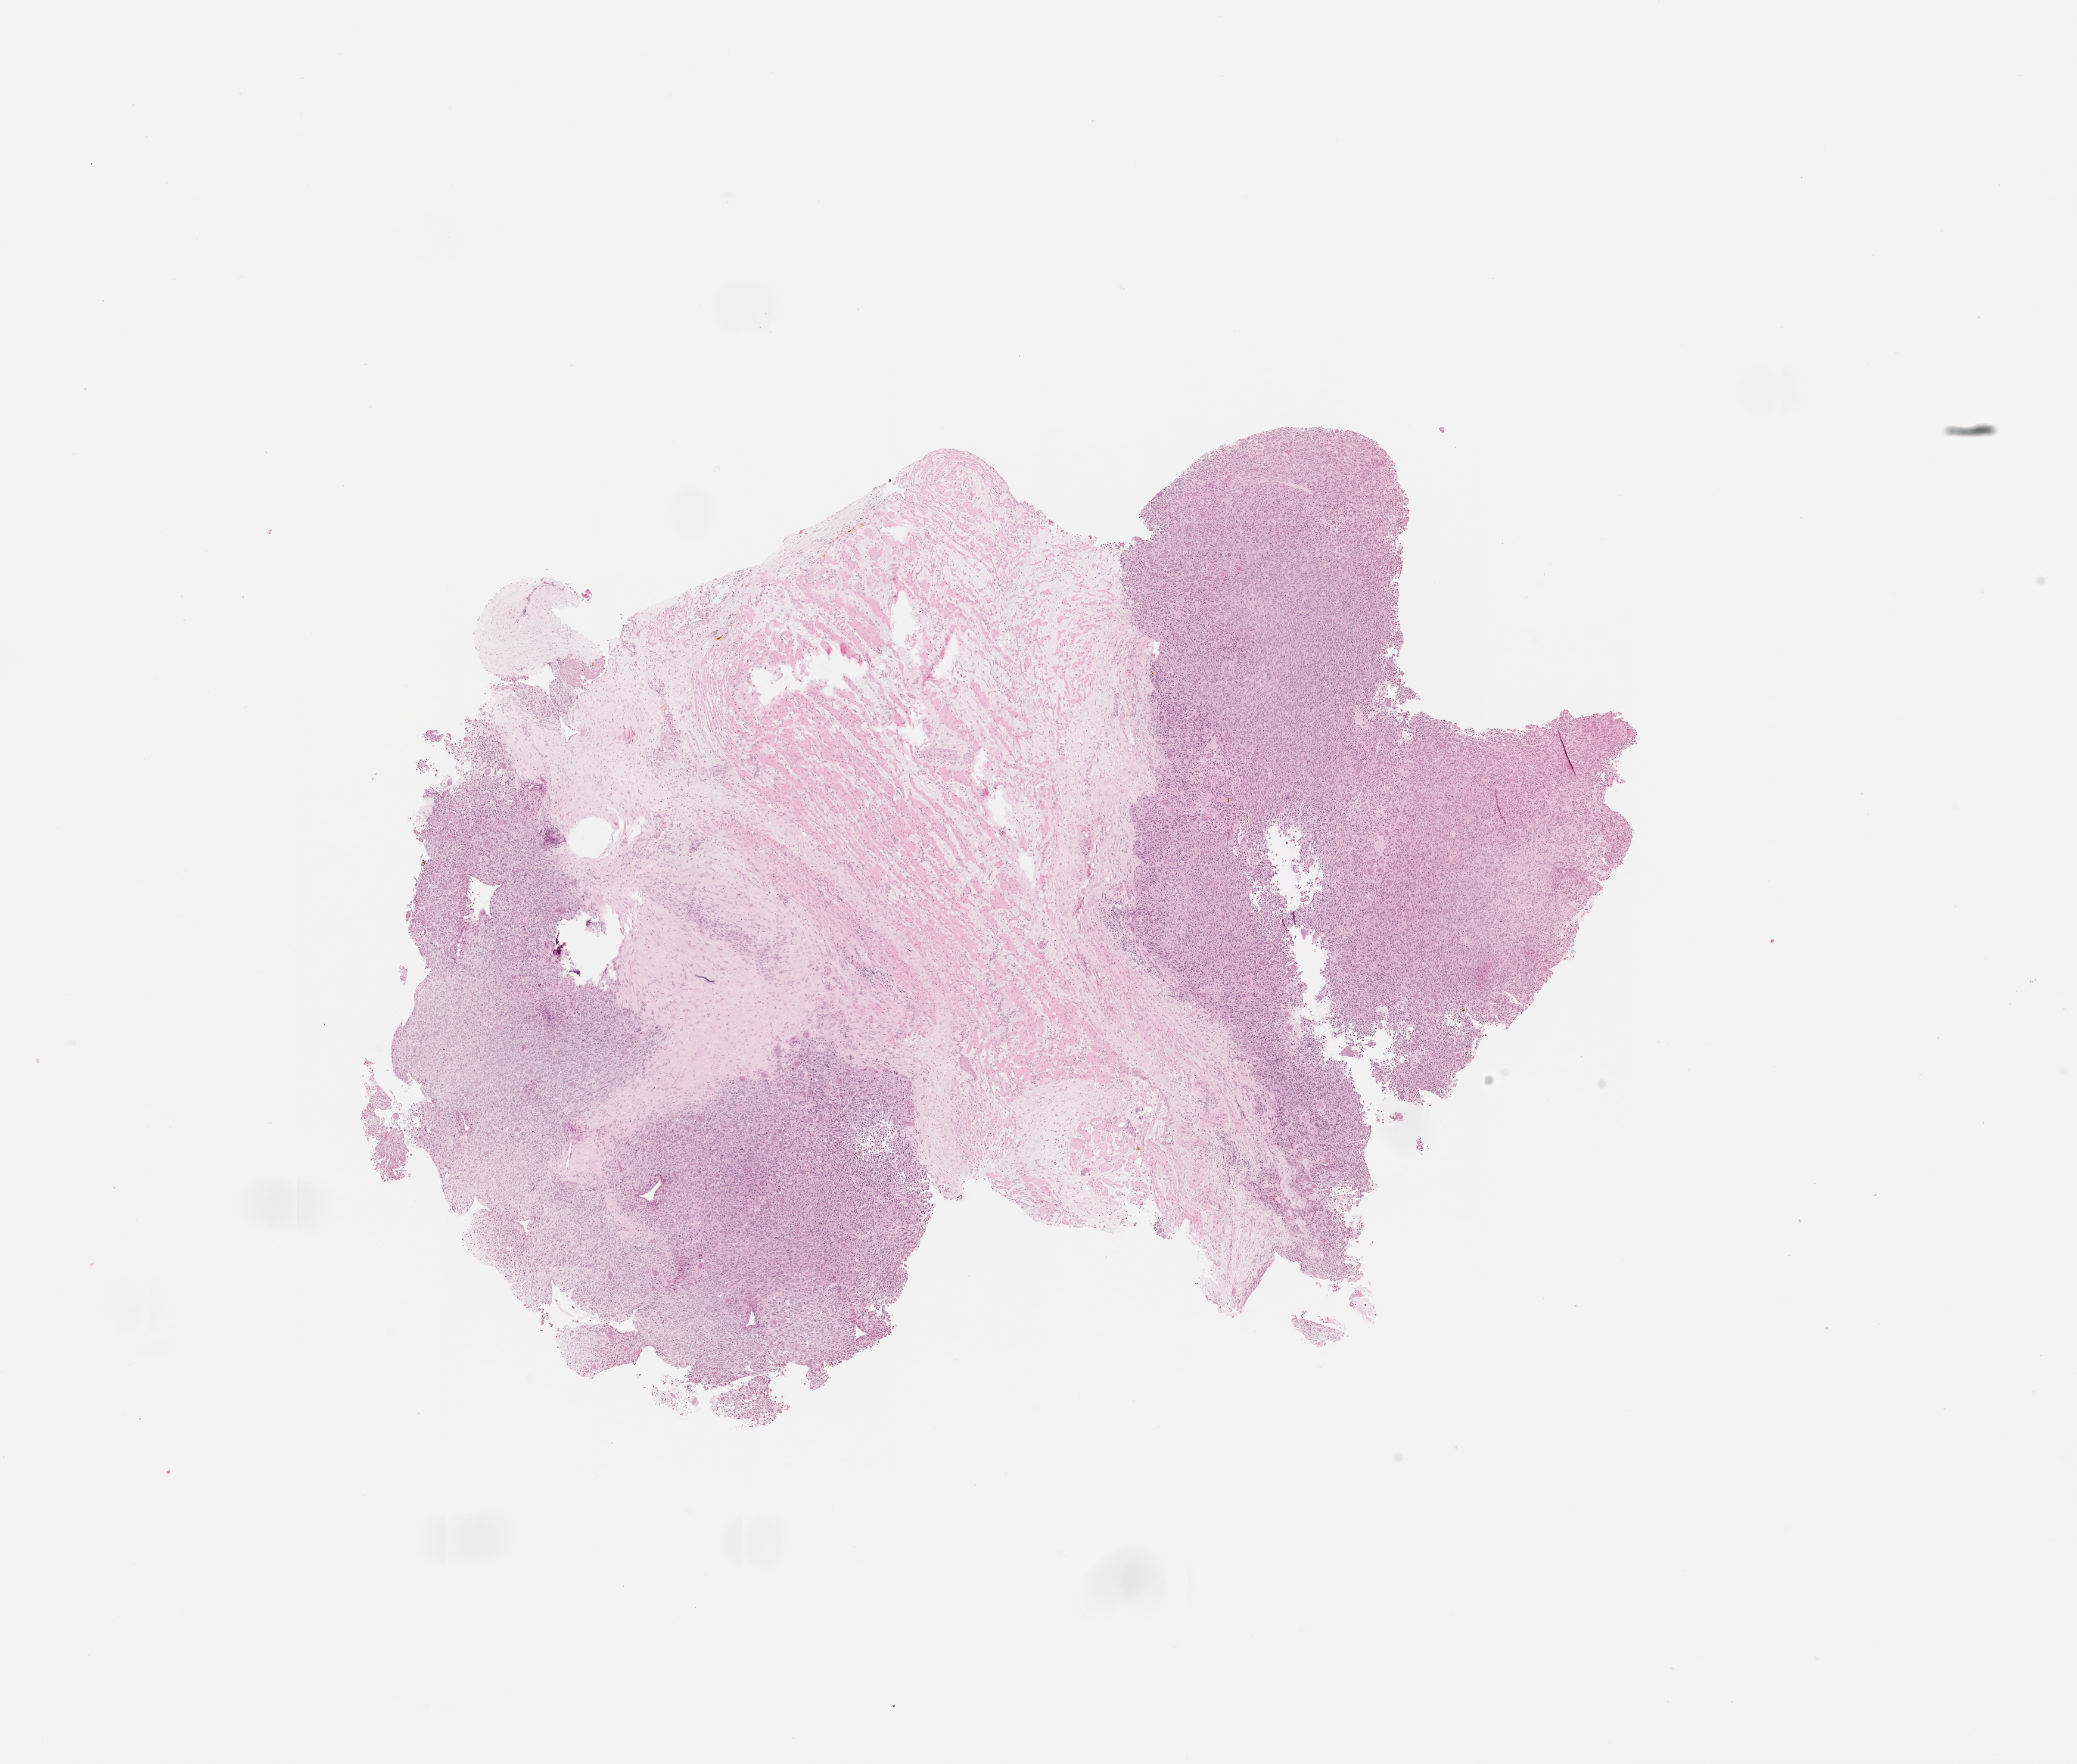
Hematoxylin and eosin (H&E) stained whole-slide image — shown as a low-resolution overview of the whole scanned area (about 14.0 x 11.9 mm, acquisition: 20x scan). Tumour tissue sample. 58-year-old female patient.
Patient diagnosis (cohort enrolment): sarcoma (site not recorded at cohort level).